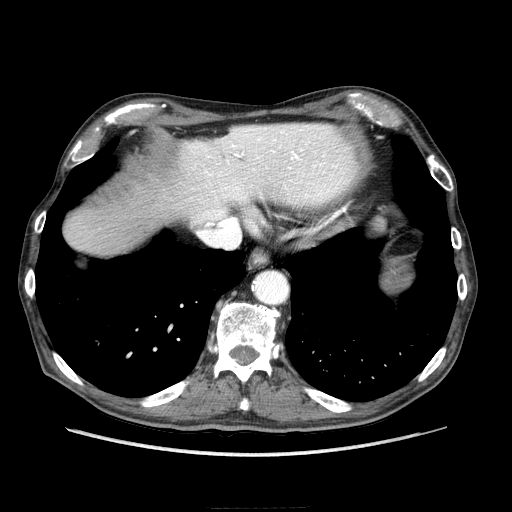
Contrast-enhanced abdominal CT (liver protocol), one axial slice. Slice 191 of 218 in the series (ordered by position). Reconstruction kernel STANDARD. 100 kVp. Soft-tissue window (W 400 / L 40 HU). 512 × 512 image matrix. From the clinical record (not read from this slice): diagnosis: hepatocellular carcinoma (patient treated with transarterial chemoembolisation; whether this scan precedes or follows treatment is not stated here); TNM stage (as recorded): Stage-IIIA; Child-Pugh class: A; tumour differentiation: well differentiated; tumour size: 20 cm.
Outlined on this slice (semi-automatic segmentation, software-assisted and operator-edited):
- liver parenchyma outside the tumour (the mass and vessels are separate outlines, so this box may not span the whole liver): bounding box [x1, y1, x2, y2] px = [64, 124, 358, 254]
- liver vessels: [188, 125, 349, 223]